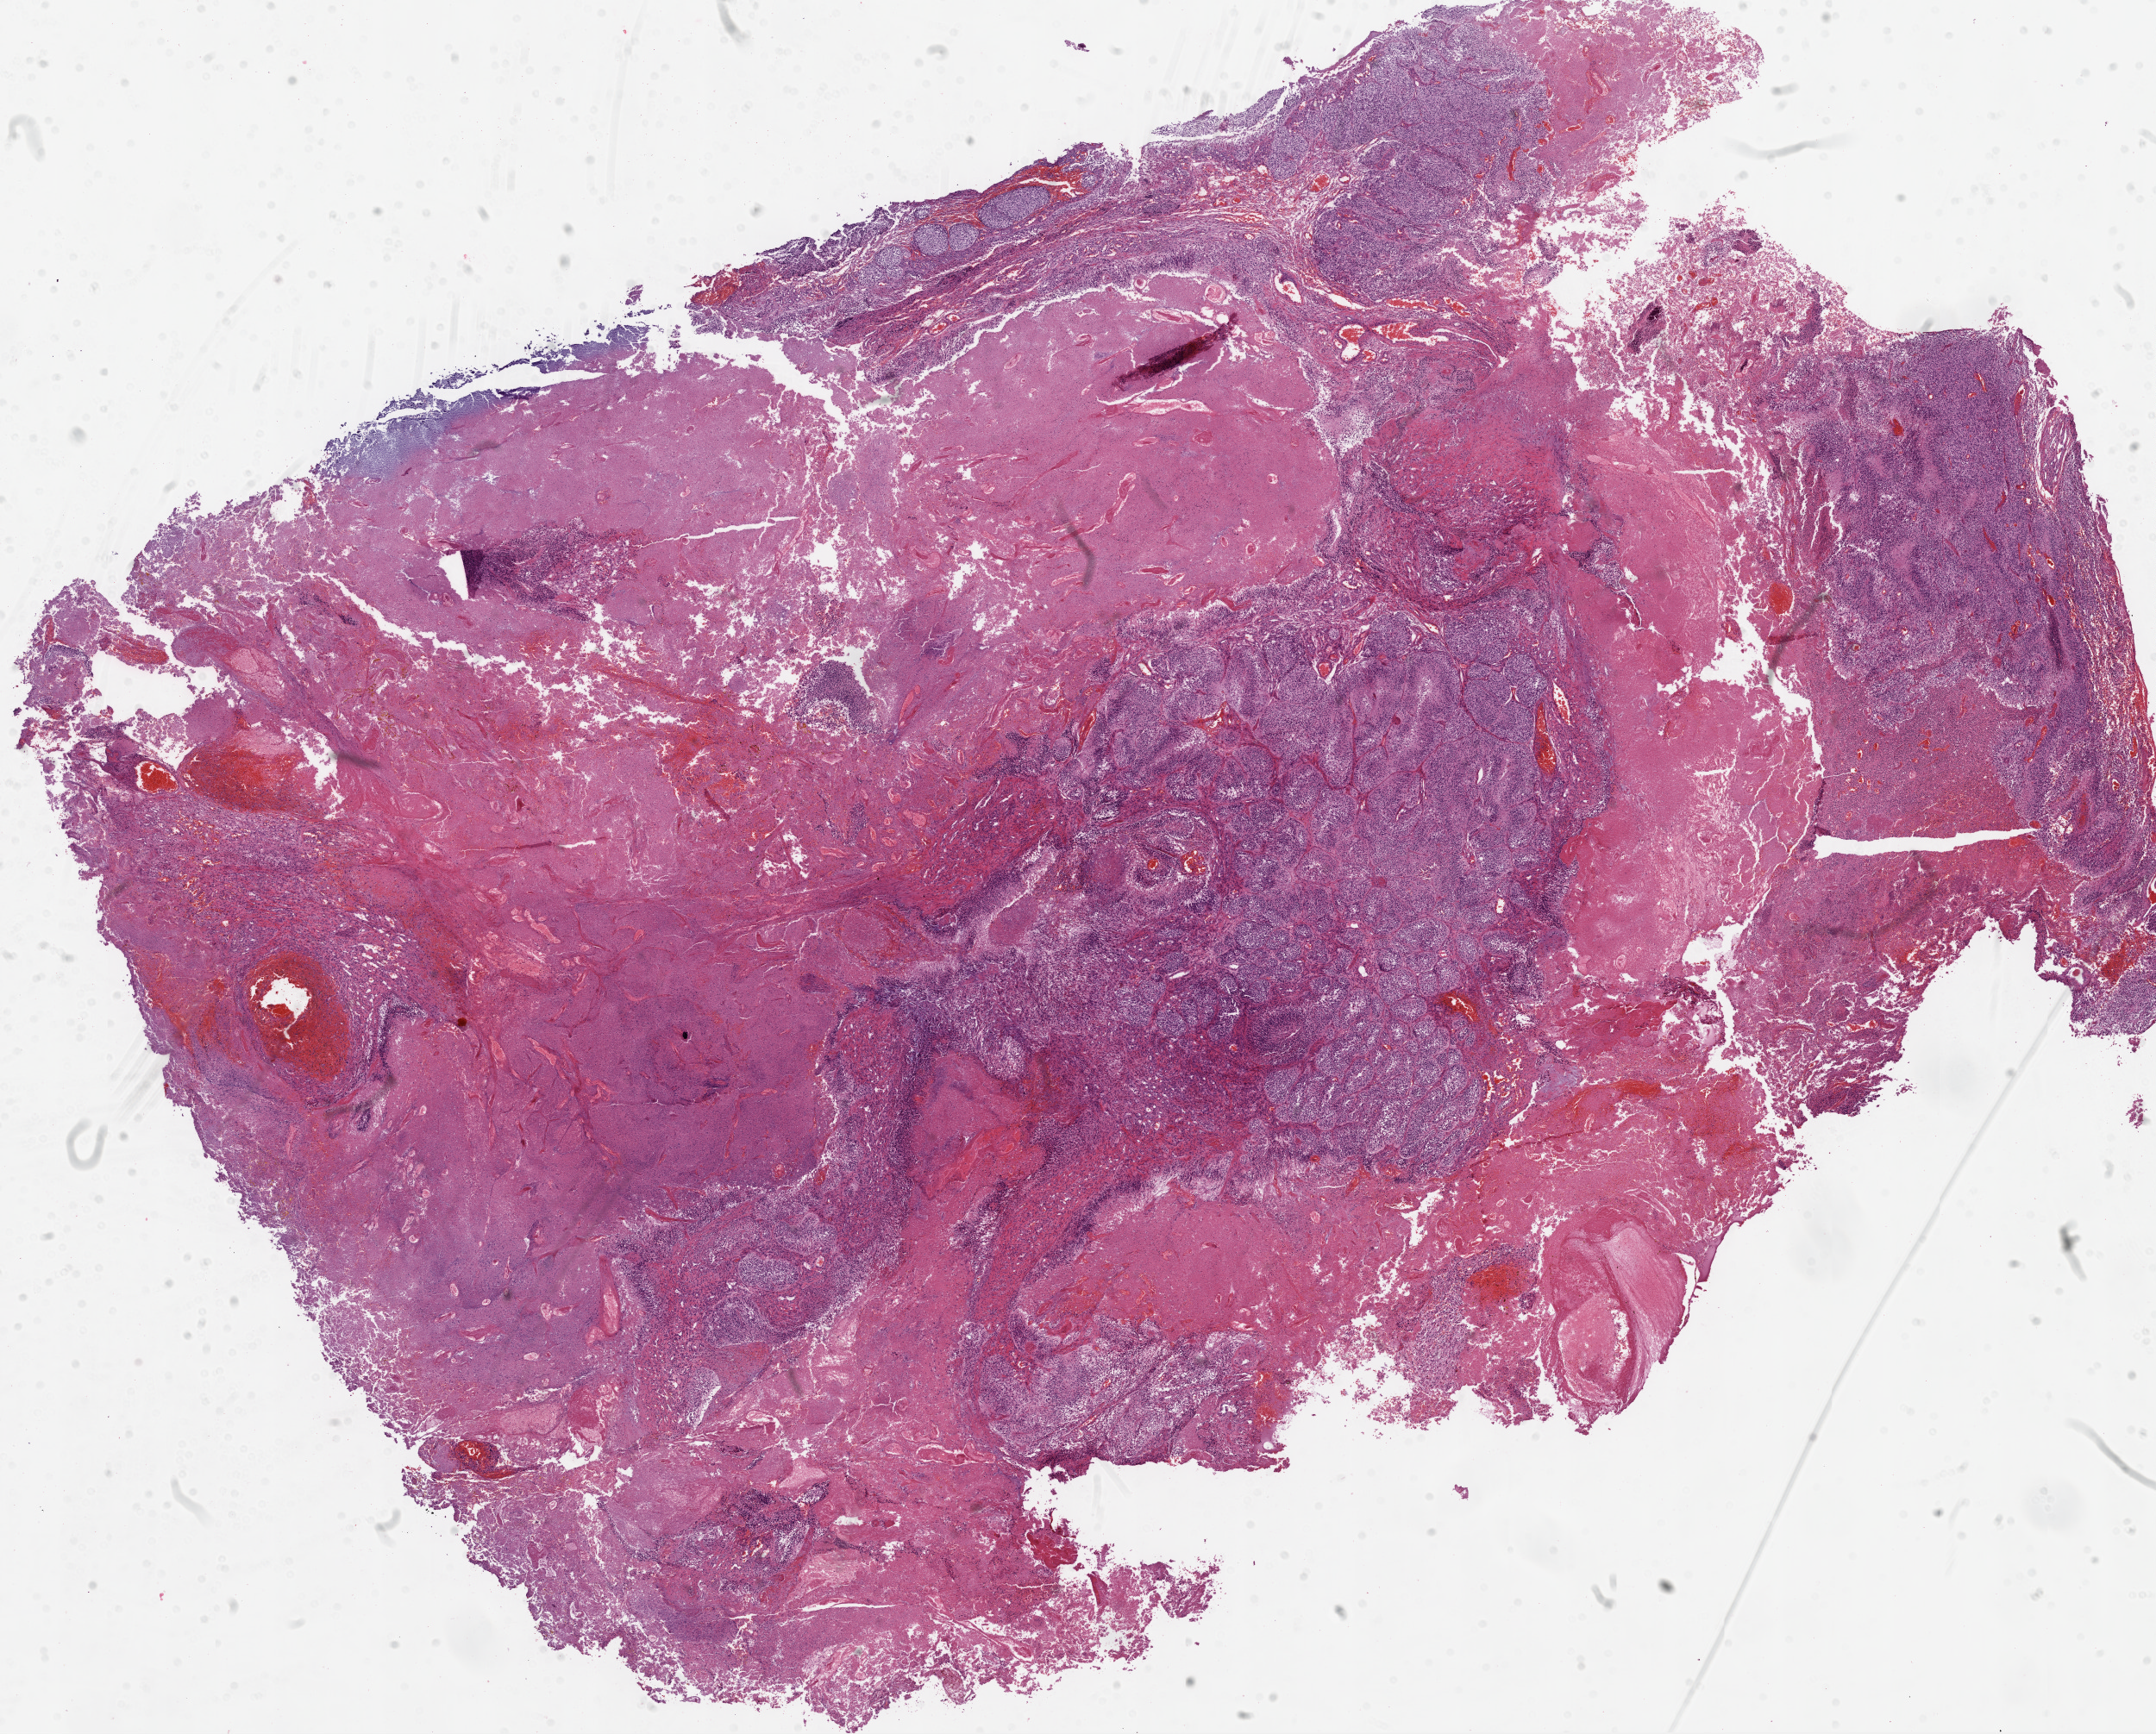
Digitized H&E-stained tissue section (whole slide) — shown as a low-resolution overview of the whole scanned area (about 20.1 x 16.1 mm); formalin-fixed paraffin-embedded (FFPE) diagnostic section; brain, primary tumour sample. Male patient; age at initial diagnosis 40 years.
Histologic diagnosis: Glioblastoma.